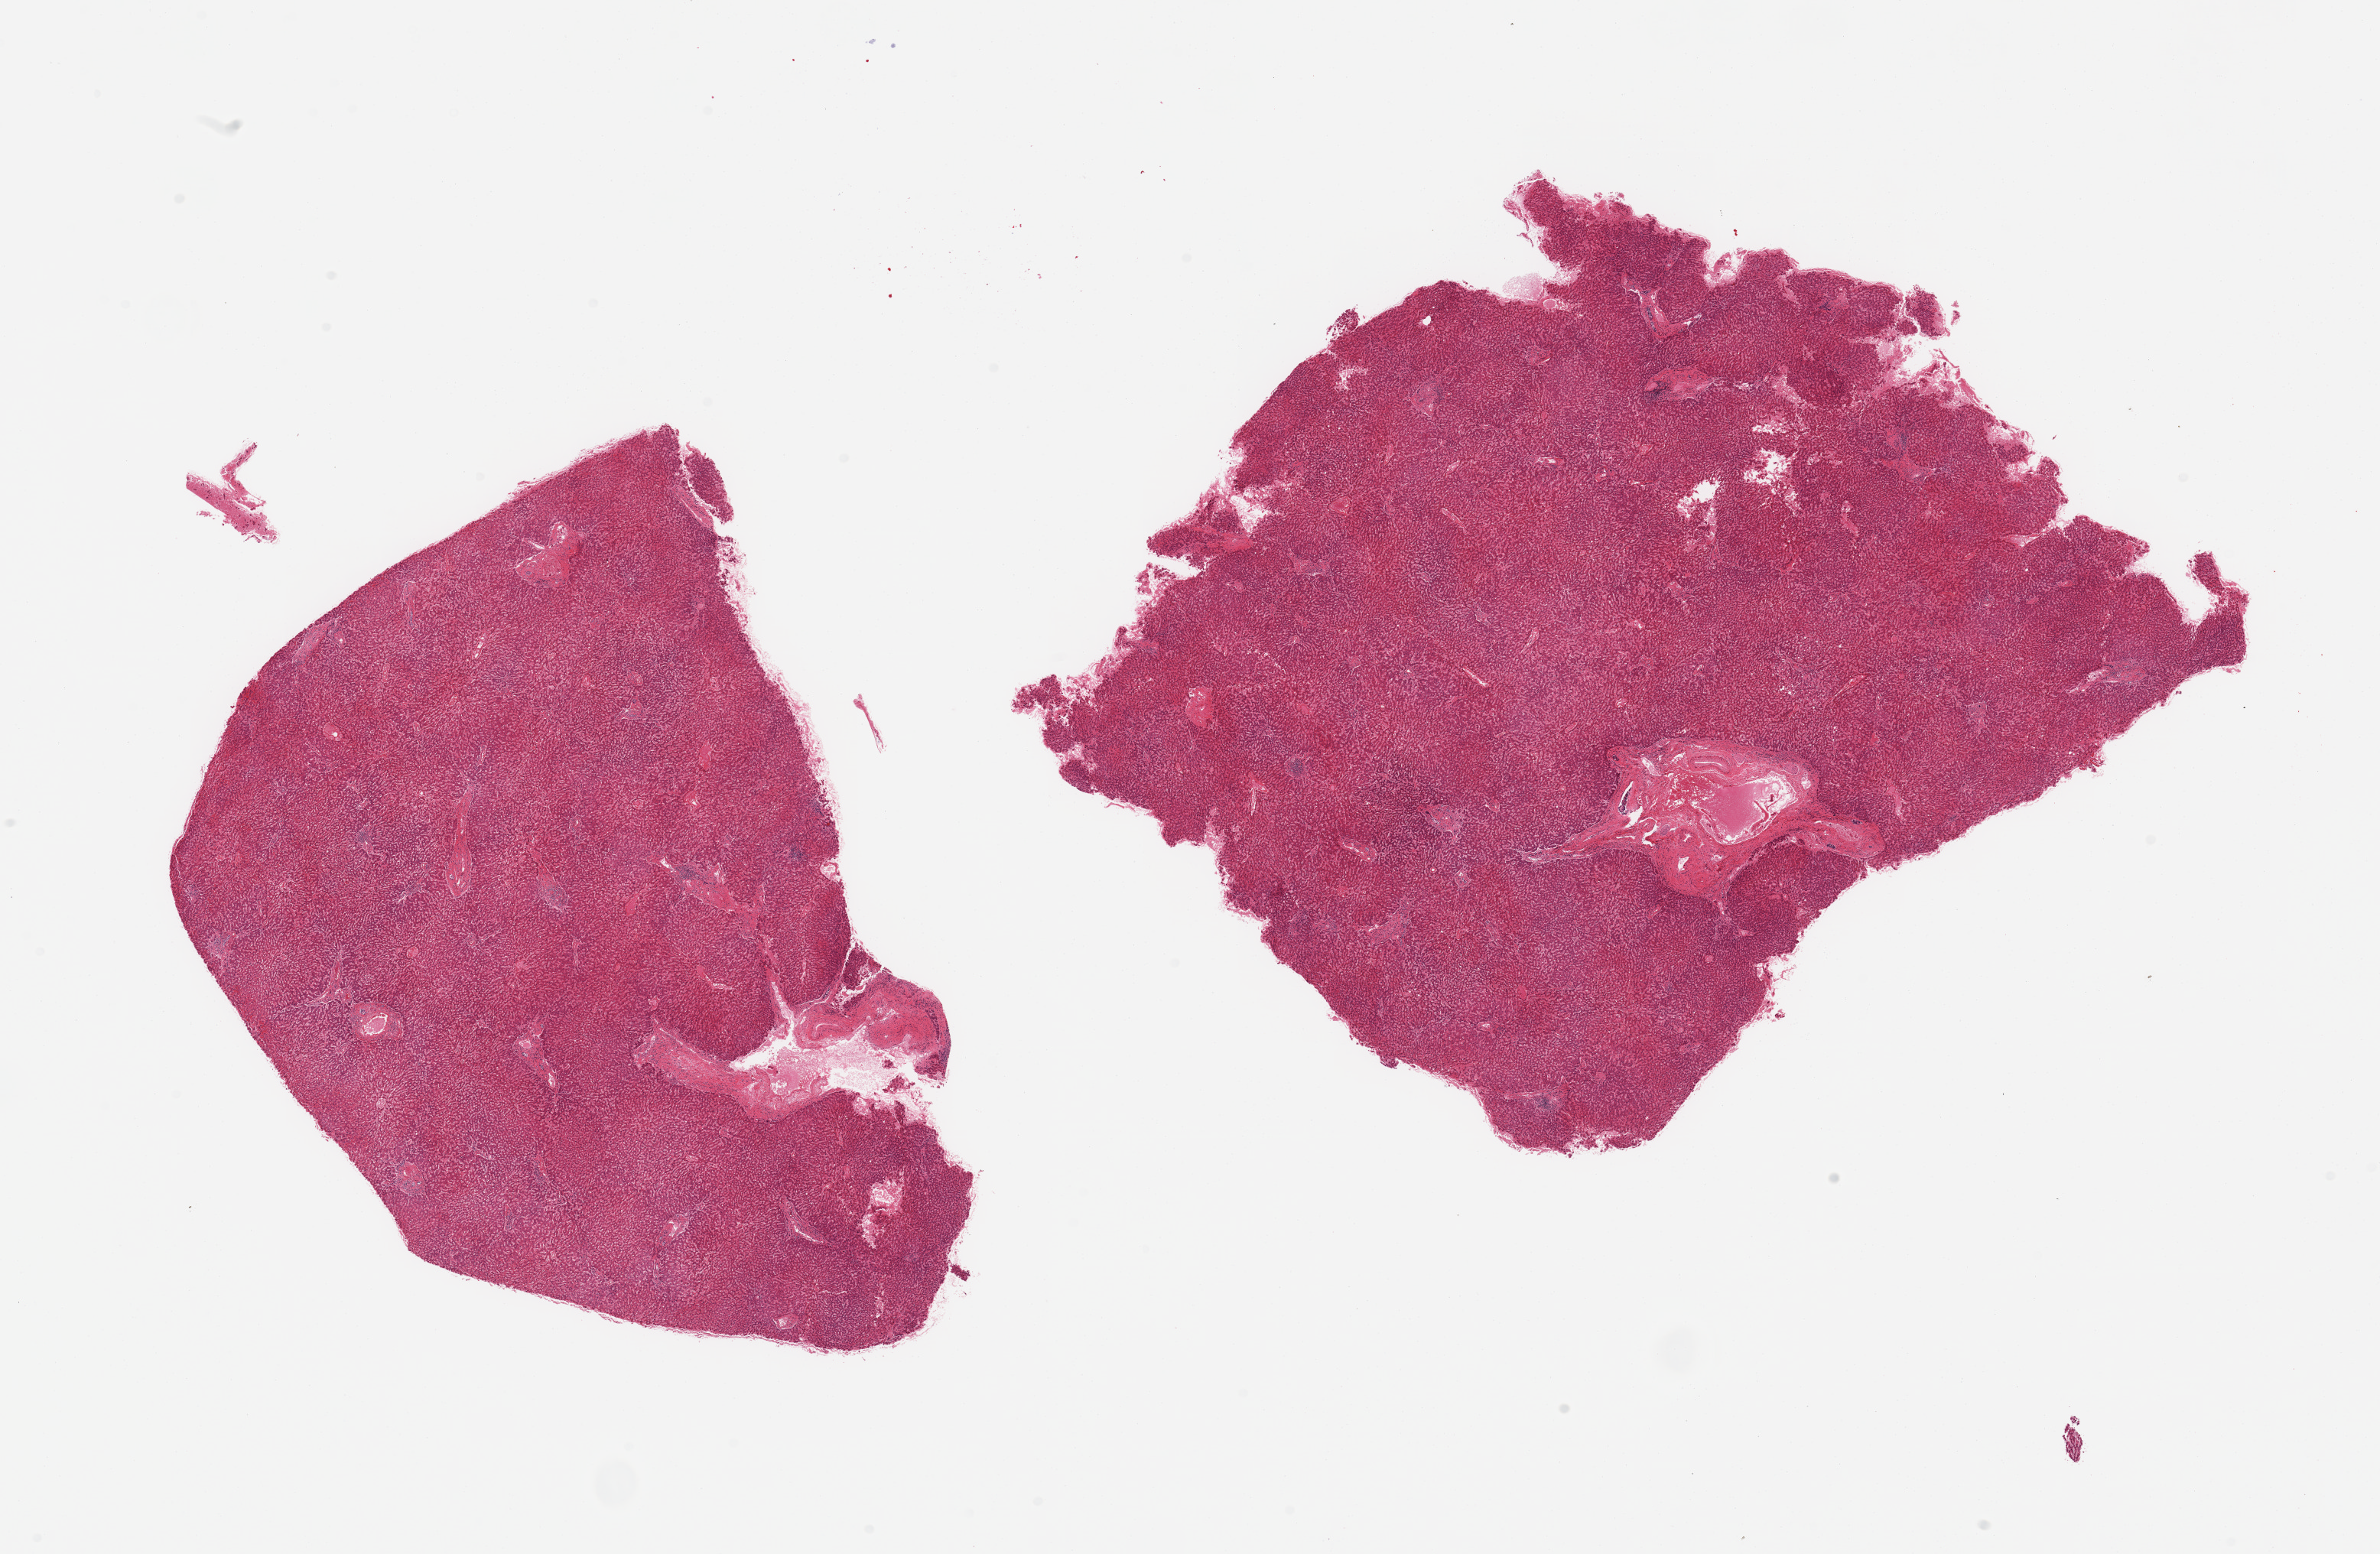
Whole-slide image, H&E stain, brightfield — low-resolution overview of the scanned area, about 24.6 x 16.1 mm. PAXgene-fixed, paraffin-embedded tissue. Target tissue: liver. Donor tissue sample. Female donor.
Reviewer comment on this tissue sample: 2 pieces; no sign of chronic passive congestion.